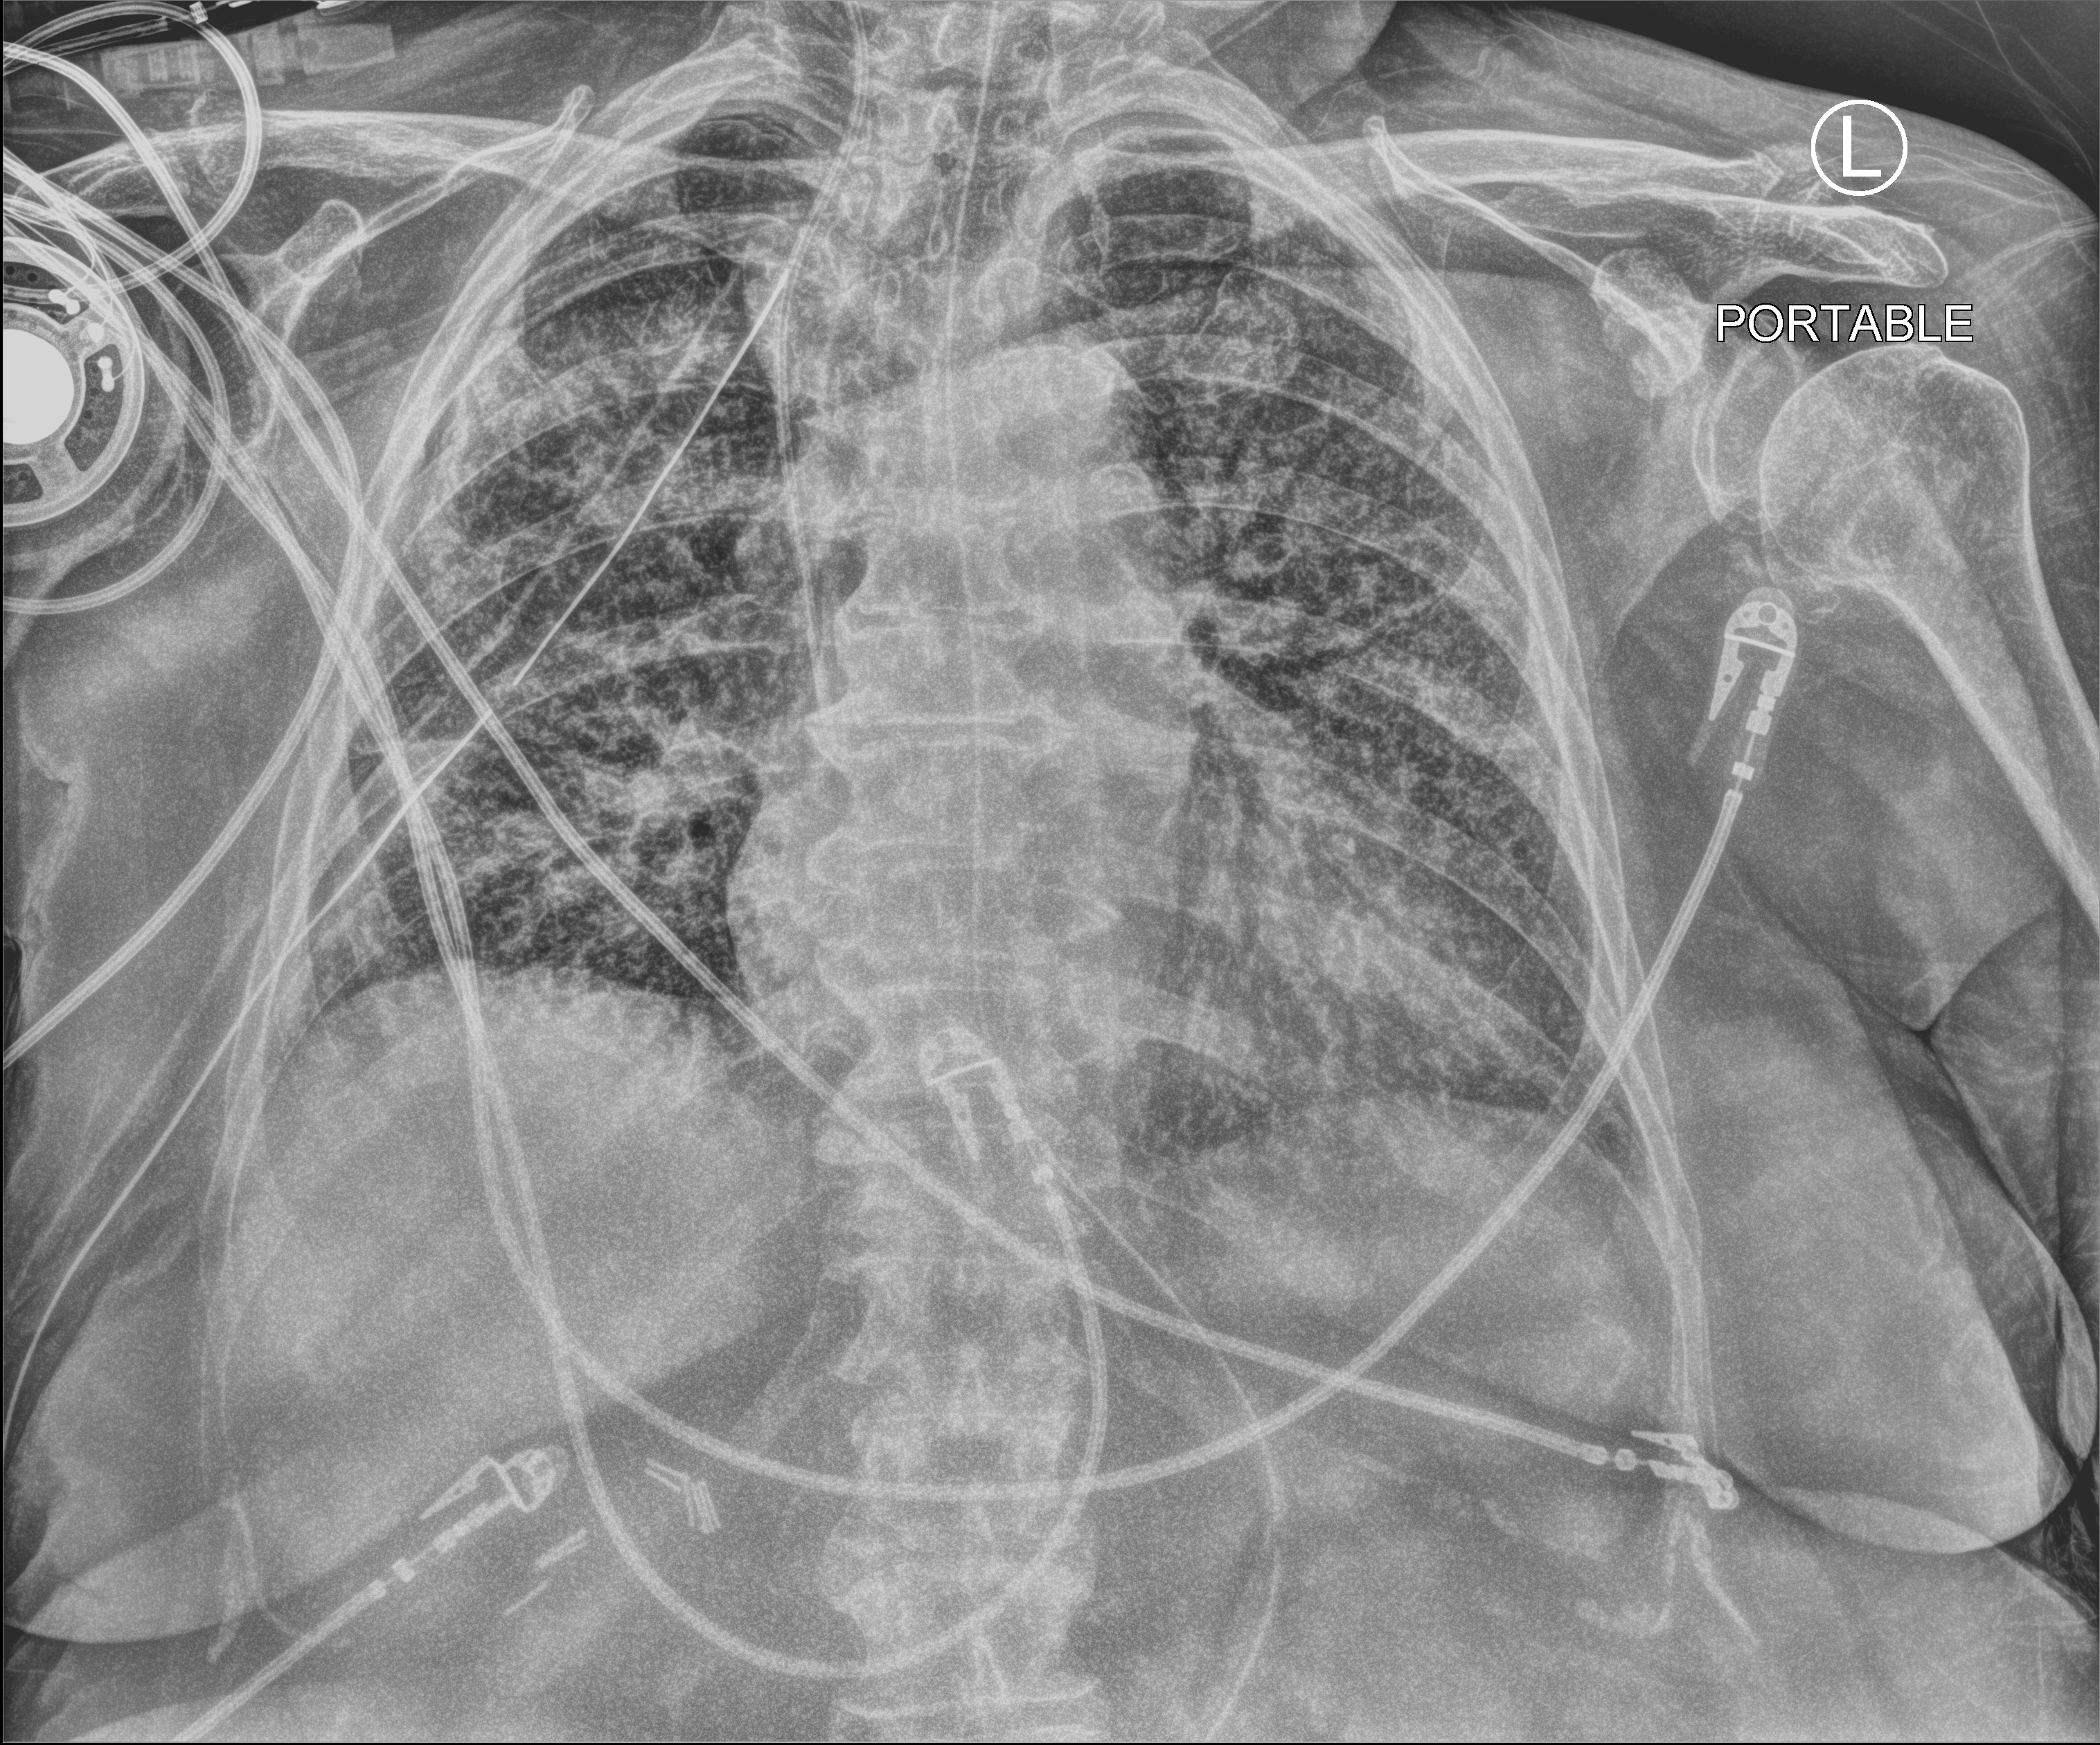
Portable chest radiograph; anteroposterior (AP) projection. Patient hospitalised with COVID-19; female, aged 75–90 years.
Admission-level facts for this patient (not findings on this image; timing relative to this image not recorded): length of hospital stay: 56 days; COPD (admission record): no; mechanically ventilated during this hospital stay: yes.